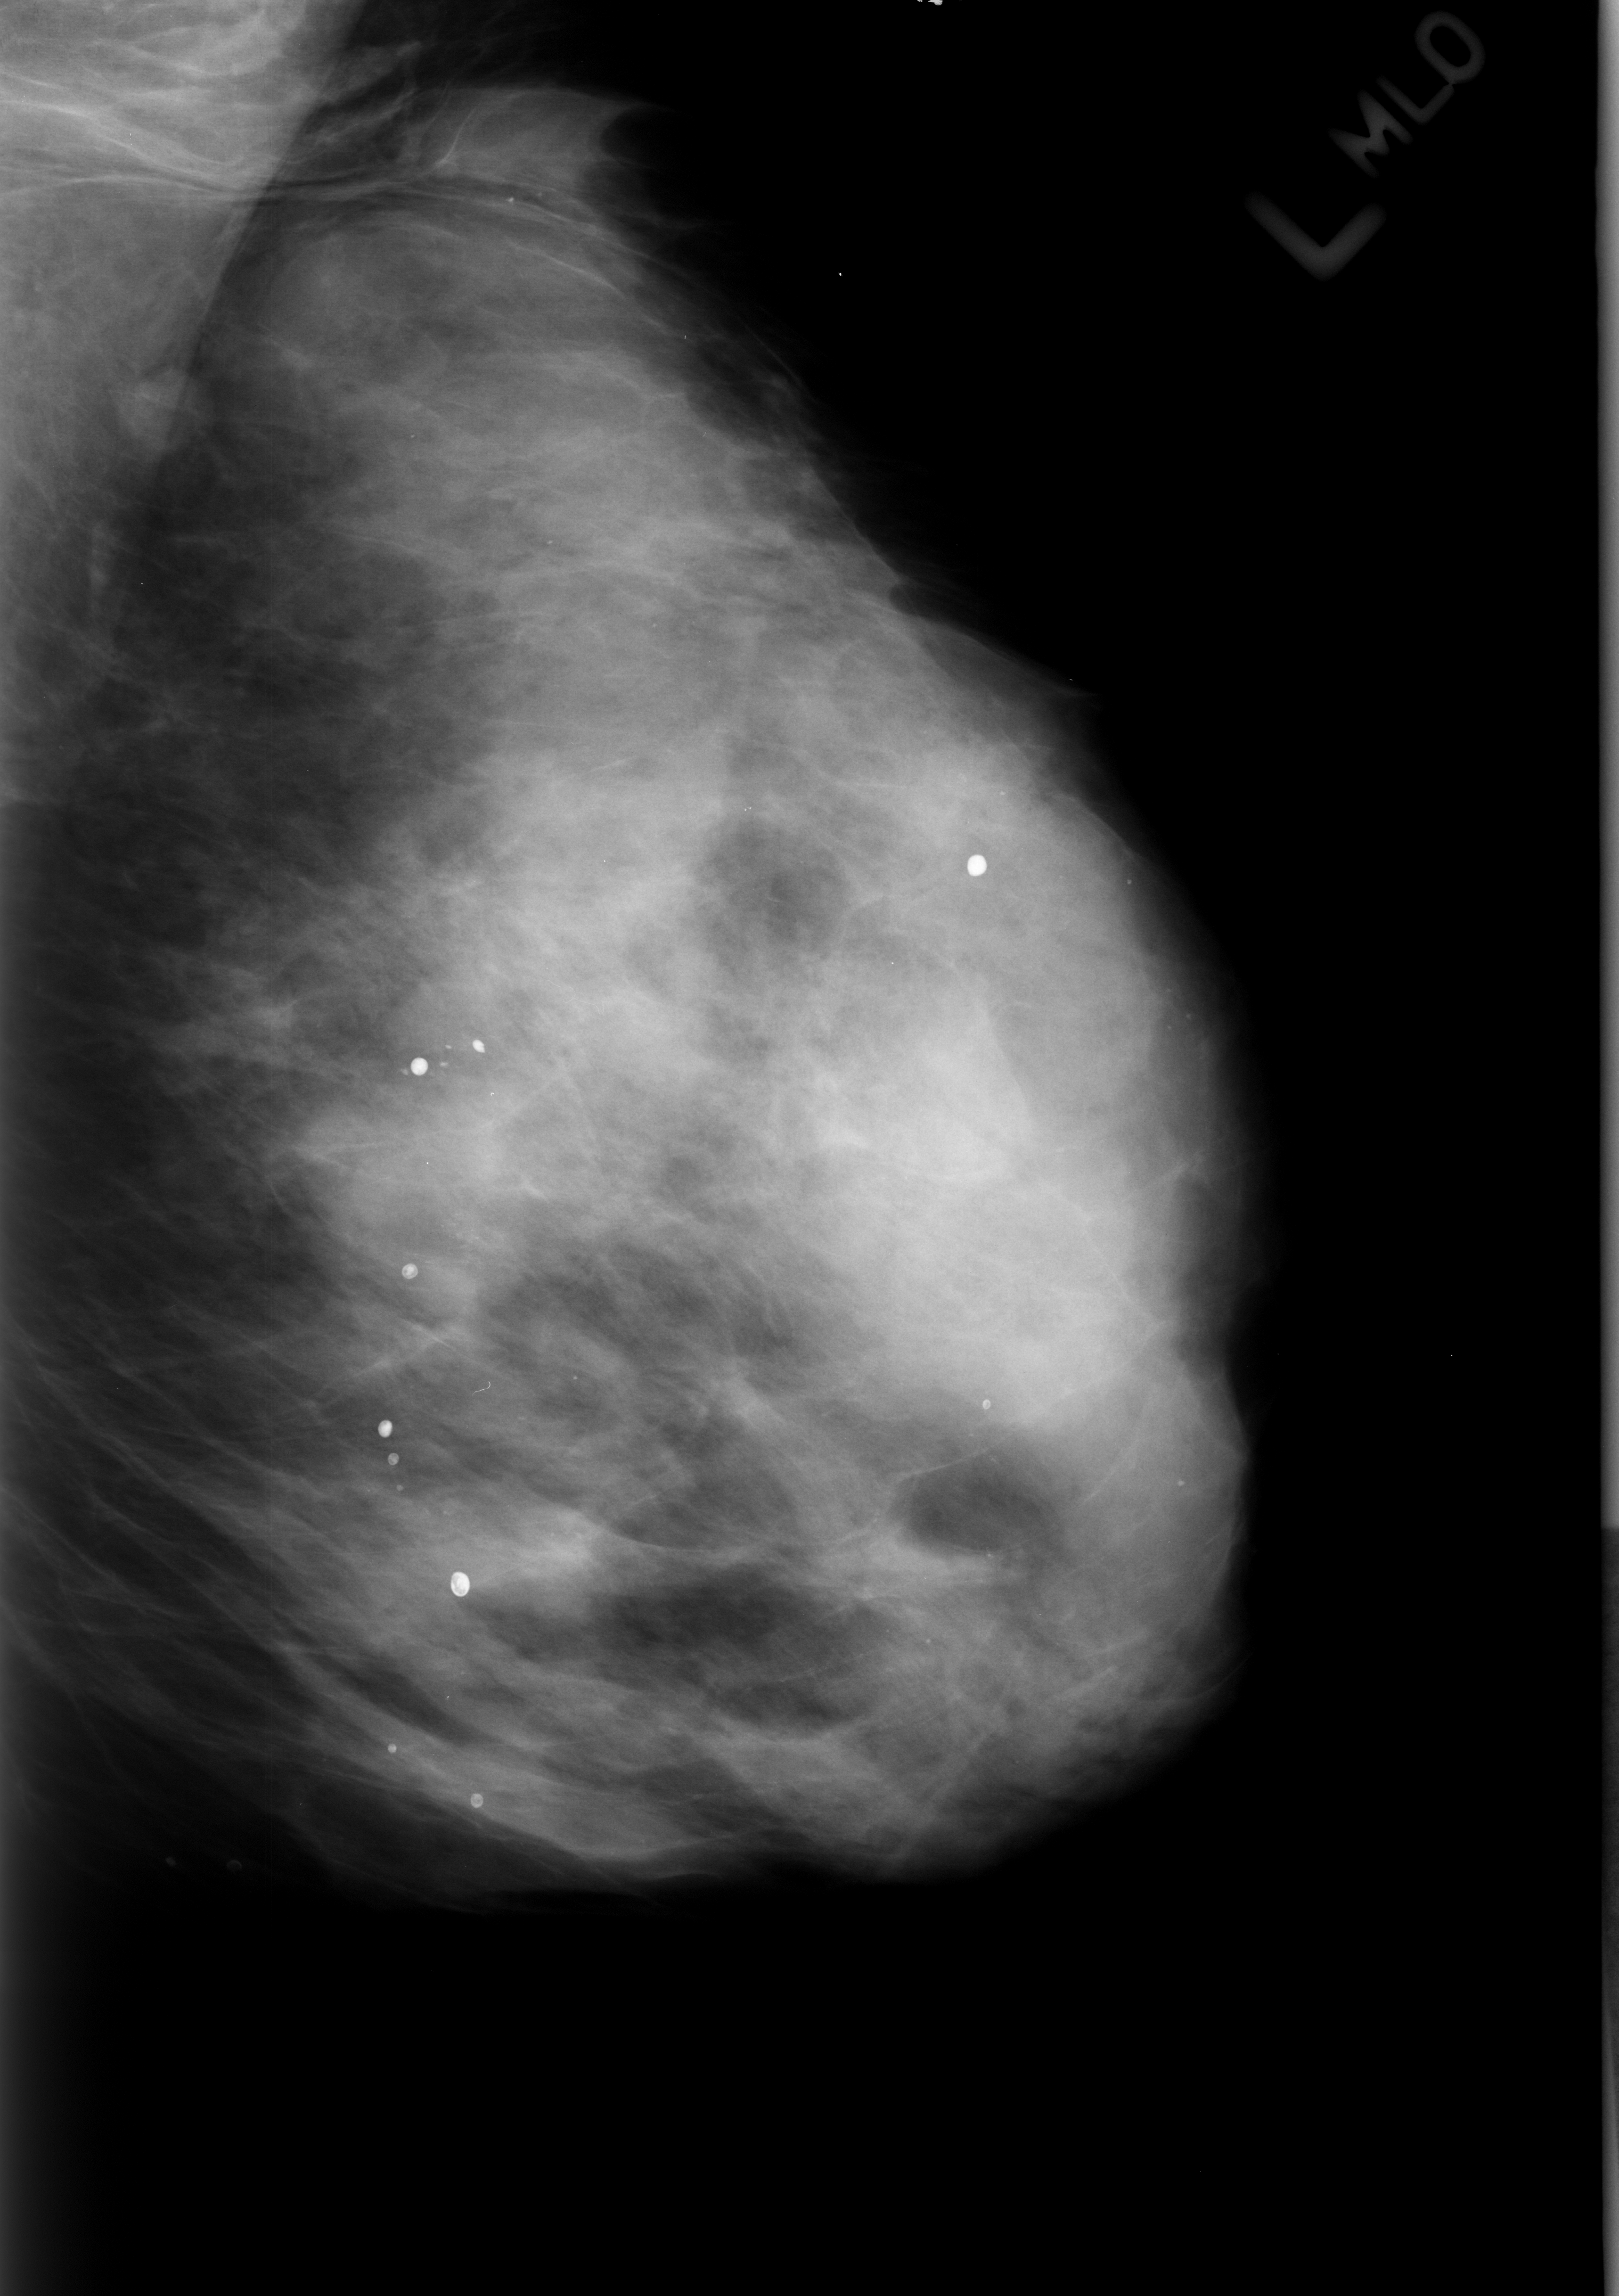
Scanned film-screen mammogram; left breast; mediolateral oblique (MLO) view; BI-RADS breast density category 4 (scale 1–4); 1619 × 2296 image matrix.
Marked abnormalities (boxes around the expert regions of interest):
- Finding 1 of 6: calcifications, morphology round and regular / lucent center / punctate, distribution diffusely scattered; BI-RADS assessment category 2; subtlety rating 5 on a 1 (subtle) to 5 (obvious) scale; benign; no additional work-up was recommended (outcome (as recorded, no biopsy): benign without callback): bounding box <370,1409,414,1441> (left, top, right, bottom; pixels)
- Finding 2 of 6: calcifications, morphology round and regular / lucent center / punctate, distribution diffusely scattered; BI-RADS assessment category 2; subtlety rating 5 on a 1 (subtle) to 5 (obvious) scale; outcome (as recorded, no biopsy): benign without callback (not worked up further): <387,1243,457,1296>
- Finding 3 of 6: calcifications, morphology round and regular / lucent center / punctate, distribution diffusely scattered; BI-RADS assessment category 2; subtlety rating 5 on a 1 (subtle) to 5 (obvious) scale; benign; no additional work-up was recommended (outcome (as recorded, no biopsy): benign without callback): <400,1039,453,1092>
- Finding 4 of 6: calcifications, morphology round and regular / lucent center / punctate, distribution diffusely scattered; BI-RADS assessment category 2; subtlety rating 5 on a 1 (subtle) to 5 (obvious) scale; outcome (as recorded, no biopsy): benign without callback (not worked up further): <430,1563,500,1611>
- Finding 5 of 6: calcifications, morphology round and regular / lucent center / punctate, distribution diffusely scattered; BI-RADS assessment category 2; subtlety rating 5 on a 1 (subtle) to 5 (obvious) scale; outcome (as recorded, no biopsy): benign without callback (not worked up further): <460,1026,508,1066>
- Finding 6 of 6: calcifications, morphology round and regular / lucent center / punctate, distribution diffusely scattered; BI-RADS assessment category 2; benign; no additional work-up was recommended (outcome (as recorded, no biopsy): benign without callback): <958,834,1011,900>